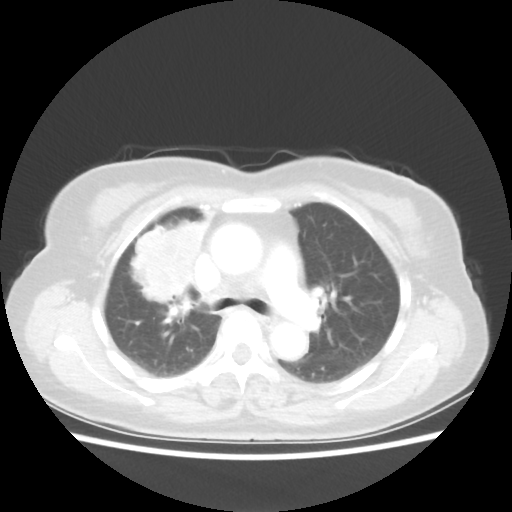
Chest CT, one axial slice; slice 35 of 55 in the series (ordered by position); 80 kVp; lung window (W 1500 / L -600 HU); 5 mm slice thickness; 512 × 512 image matrix, field of view 337 × 337 mm. Patient: female, 62 years. From the clinical record (not read from this slice): clinical TNM (as recorded): T4 N3 M0.
Structures marked on this image (rectangle marked by the reading radiologist):
- lung tumour (recorded histology: squamous cell carcinoma): bounding box (x1, y1, x2, y2) in pixels: (119, 206, 210, 298)